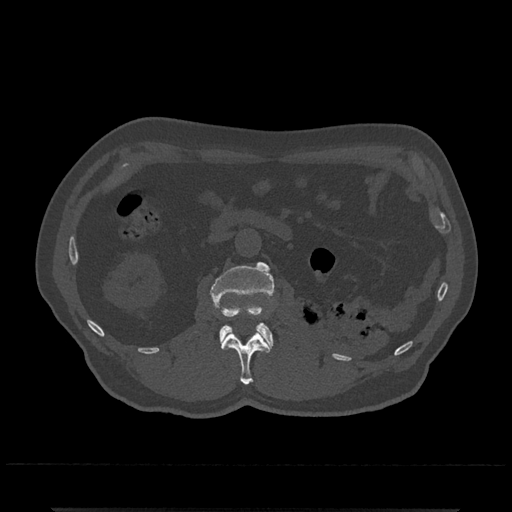
CT including the spine, one axial slice; slice 327 of 797 in the series (ordered by position); reconstruction kernel Br40s/3; 120 kVp; bone window (W 1800 / L 400 HU); 0.5 mm slice thickness; 512 × 512 image matrix. Patient: male, 67 years. From the clinical record (not read from this slice): primary cancer: prostate.
Outlined on this slice (semi-automatic segmentation, software-assisted and operator-edited):
- L1 vertebra: bounding box <221,331,270,385> (left, top, right, bottom; pixels)
- L2 vertebra: <210,262,275,351>